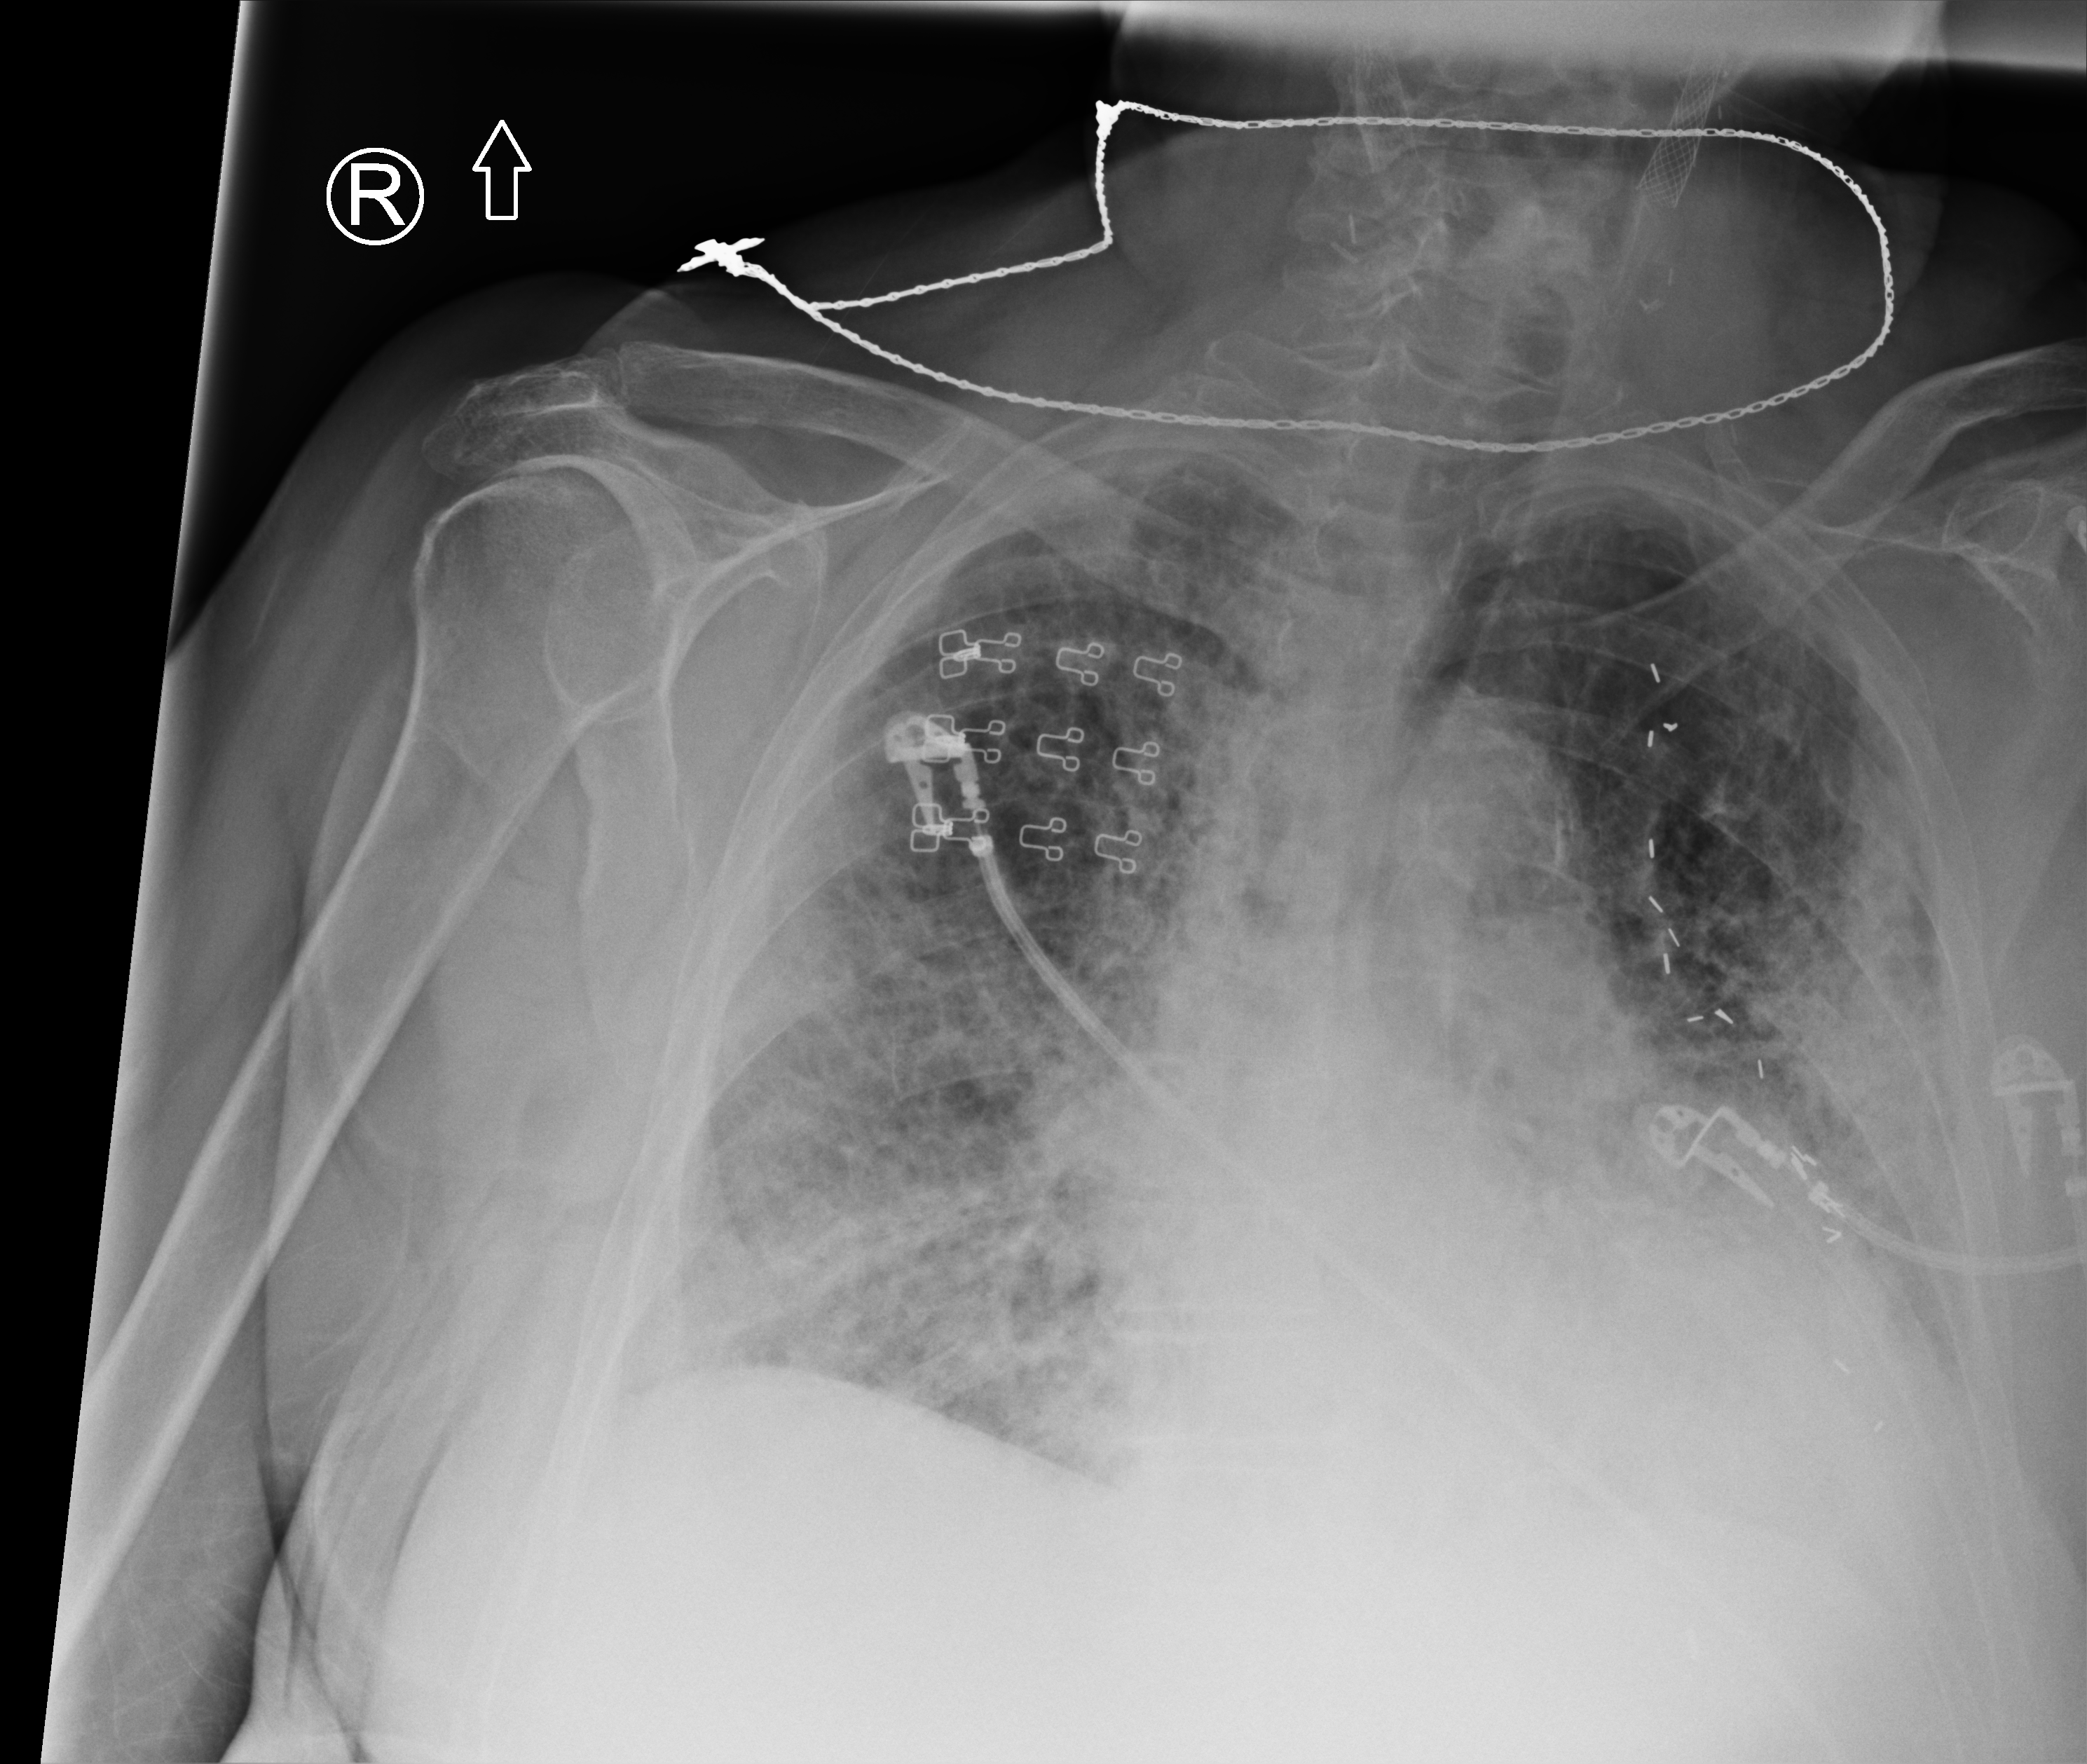
Bedside chest radiograph (computed radiography). Female patient hospitalised with COVID-19, age 75–90 years.
From the hospital-stay record, not from the radiograph (when in the stay this image was taken is not recorded):
- admitted to intensive care during this hospital stay: no
- length of hospital stay: 3 days
- mechanically ventilated during this hospital stay: no